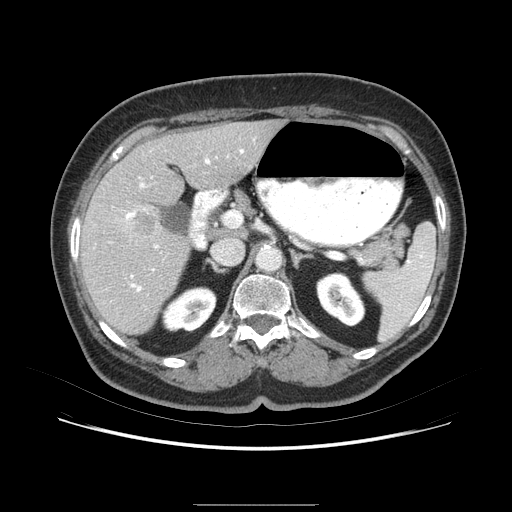
Contrast-enhanced abdominal CT (liver protocol), one axial slice; slice 42 of 79 in the series (ordered by position); soft-tissue window (W 400 / L 40 HU); 2.5 mm slice thickness; 512 × 512 image matrix, field of view 380 × 380 mm. Case-level facts recorded for this patient, not image findings: diagnosis: hepatocellular carcinoma (patient treated with transarterial chemoembolisation; whether this scan precedes or follows treatment is not stated here); TNM stage (as recorded): Stage-I; Child-Pugh class: A; tumour differentiation: poorly differentiated.
Structures marked on this image (semi-automatic segmentation, software-assisted and operator-edited):
- liver parenchyma outside the tumour (the mass and vessels are separate outlines, so this box may not span the whole liver): bounding box [x1, y1, x2, y2] px = [80, 122, 288, 342]
- mass: [124, 204, 170, 245]
- liver vessels: [114, 147, 260, 292]